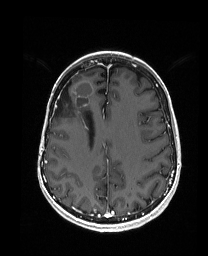
Brain MRI from a brain-tumour surgery series, one axial slice. Slice 66 of 192 in the series (ordered by position). T1-weighted post-contrast. 1 mm slice thickness. 208 × 256 image matrix, field of view 203 × 250 mm. From the clinical record (not read from this slice): histopathology: Metastatic Carcinoma from Breast primary; tumour location: Right Frontal.
Annotated regions visible in this slice (outlined manually by an expert reader):
- previous resection cavity: bounding box <54,82,71,115> (left, top, right, bottom; pixels)
- tumour: <79,80,101,115>